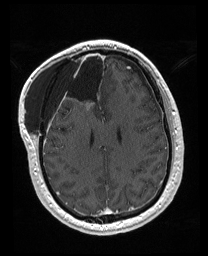
Brain MRI from a brain-tumour surgery series, one axial slice; position 67 of 176 along the scan axis; T1-weighted post-contrast; 1 mm slice thickness; 208 × 256 image matrix, field of view 208 × 256 mm. Case-level facts recorded for this patient, not image findings: histopathology: Astrocytoma; WHO grade: 4; IDH mutation: yes.
Annotated regions visible in this slice (manually delineated by an expert):
- previous resection cavity: bounding box (x1, y1, x2, y2) in pixels: (60, 52, 97, 111)